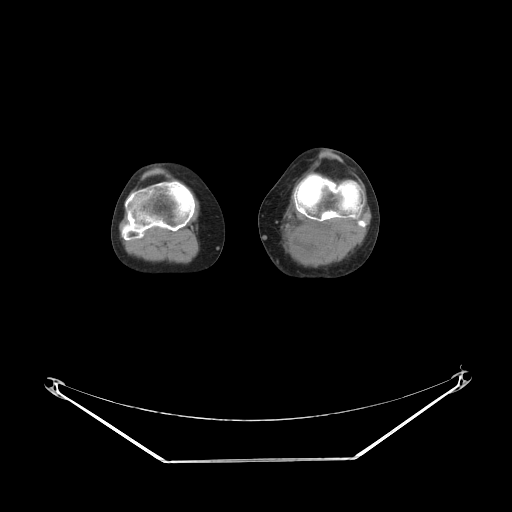
CT of an extremity soft-tissue mass (from a PET/CT study), one axial slice. Position 162 of 223 along the scan axis. Soft-tissue window (W 400 / L 40 HU). 3.75 mm slice thickness. 512 × 512 image matrix, field of view 500 × 500 mm. Female patient. From the clinical record (not read from this slice): histological type: extraskeletal high grade osteogenic sarcoma; grade: high; site of the primary tumour: left calf.
Structures marked on this image (expert contour drawn on MRI and transferred to this co-registered scan by the dataset authors):
- gross tumour volume (mass): bounding box [x1, y1, x2, y2] px = [290, 230, 323, 257]